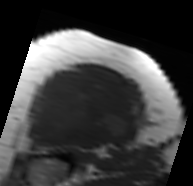
MRI of an extremity soft-tissue mass, one axial slice; position 55 of 91 along the scan axis; MR volume resampled by the dataset authors to the PET/CT grid (not the native acquisition matrix); 3.27 mm slice thickness; 193 × 186 image matrix, field of view 188 × 182 mm. Female patient. From the clinical record (not read from this slice): histological type: malignant solitary fibrous tumor; grade: intermediate; site of the primary tumour: right thigh.
Structures marked on this image (expert contour drawn on MRI and transferred to this co-registered scan by the dataset authors):
- gross tumour volume including surrounding oedema: box from (x=28, y=69) to (x=139, y=148) px
- gross tumour volume (mass): (x=28, y=71)–(x=137, y=148)